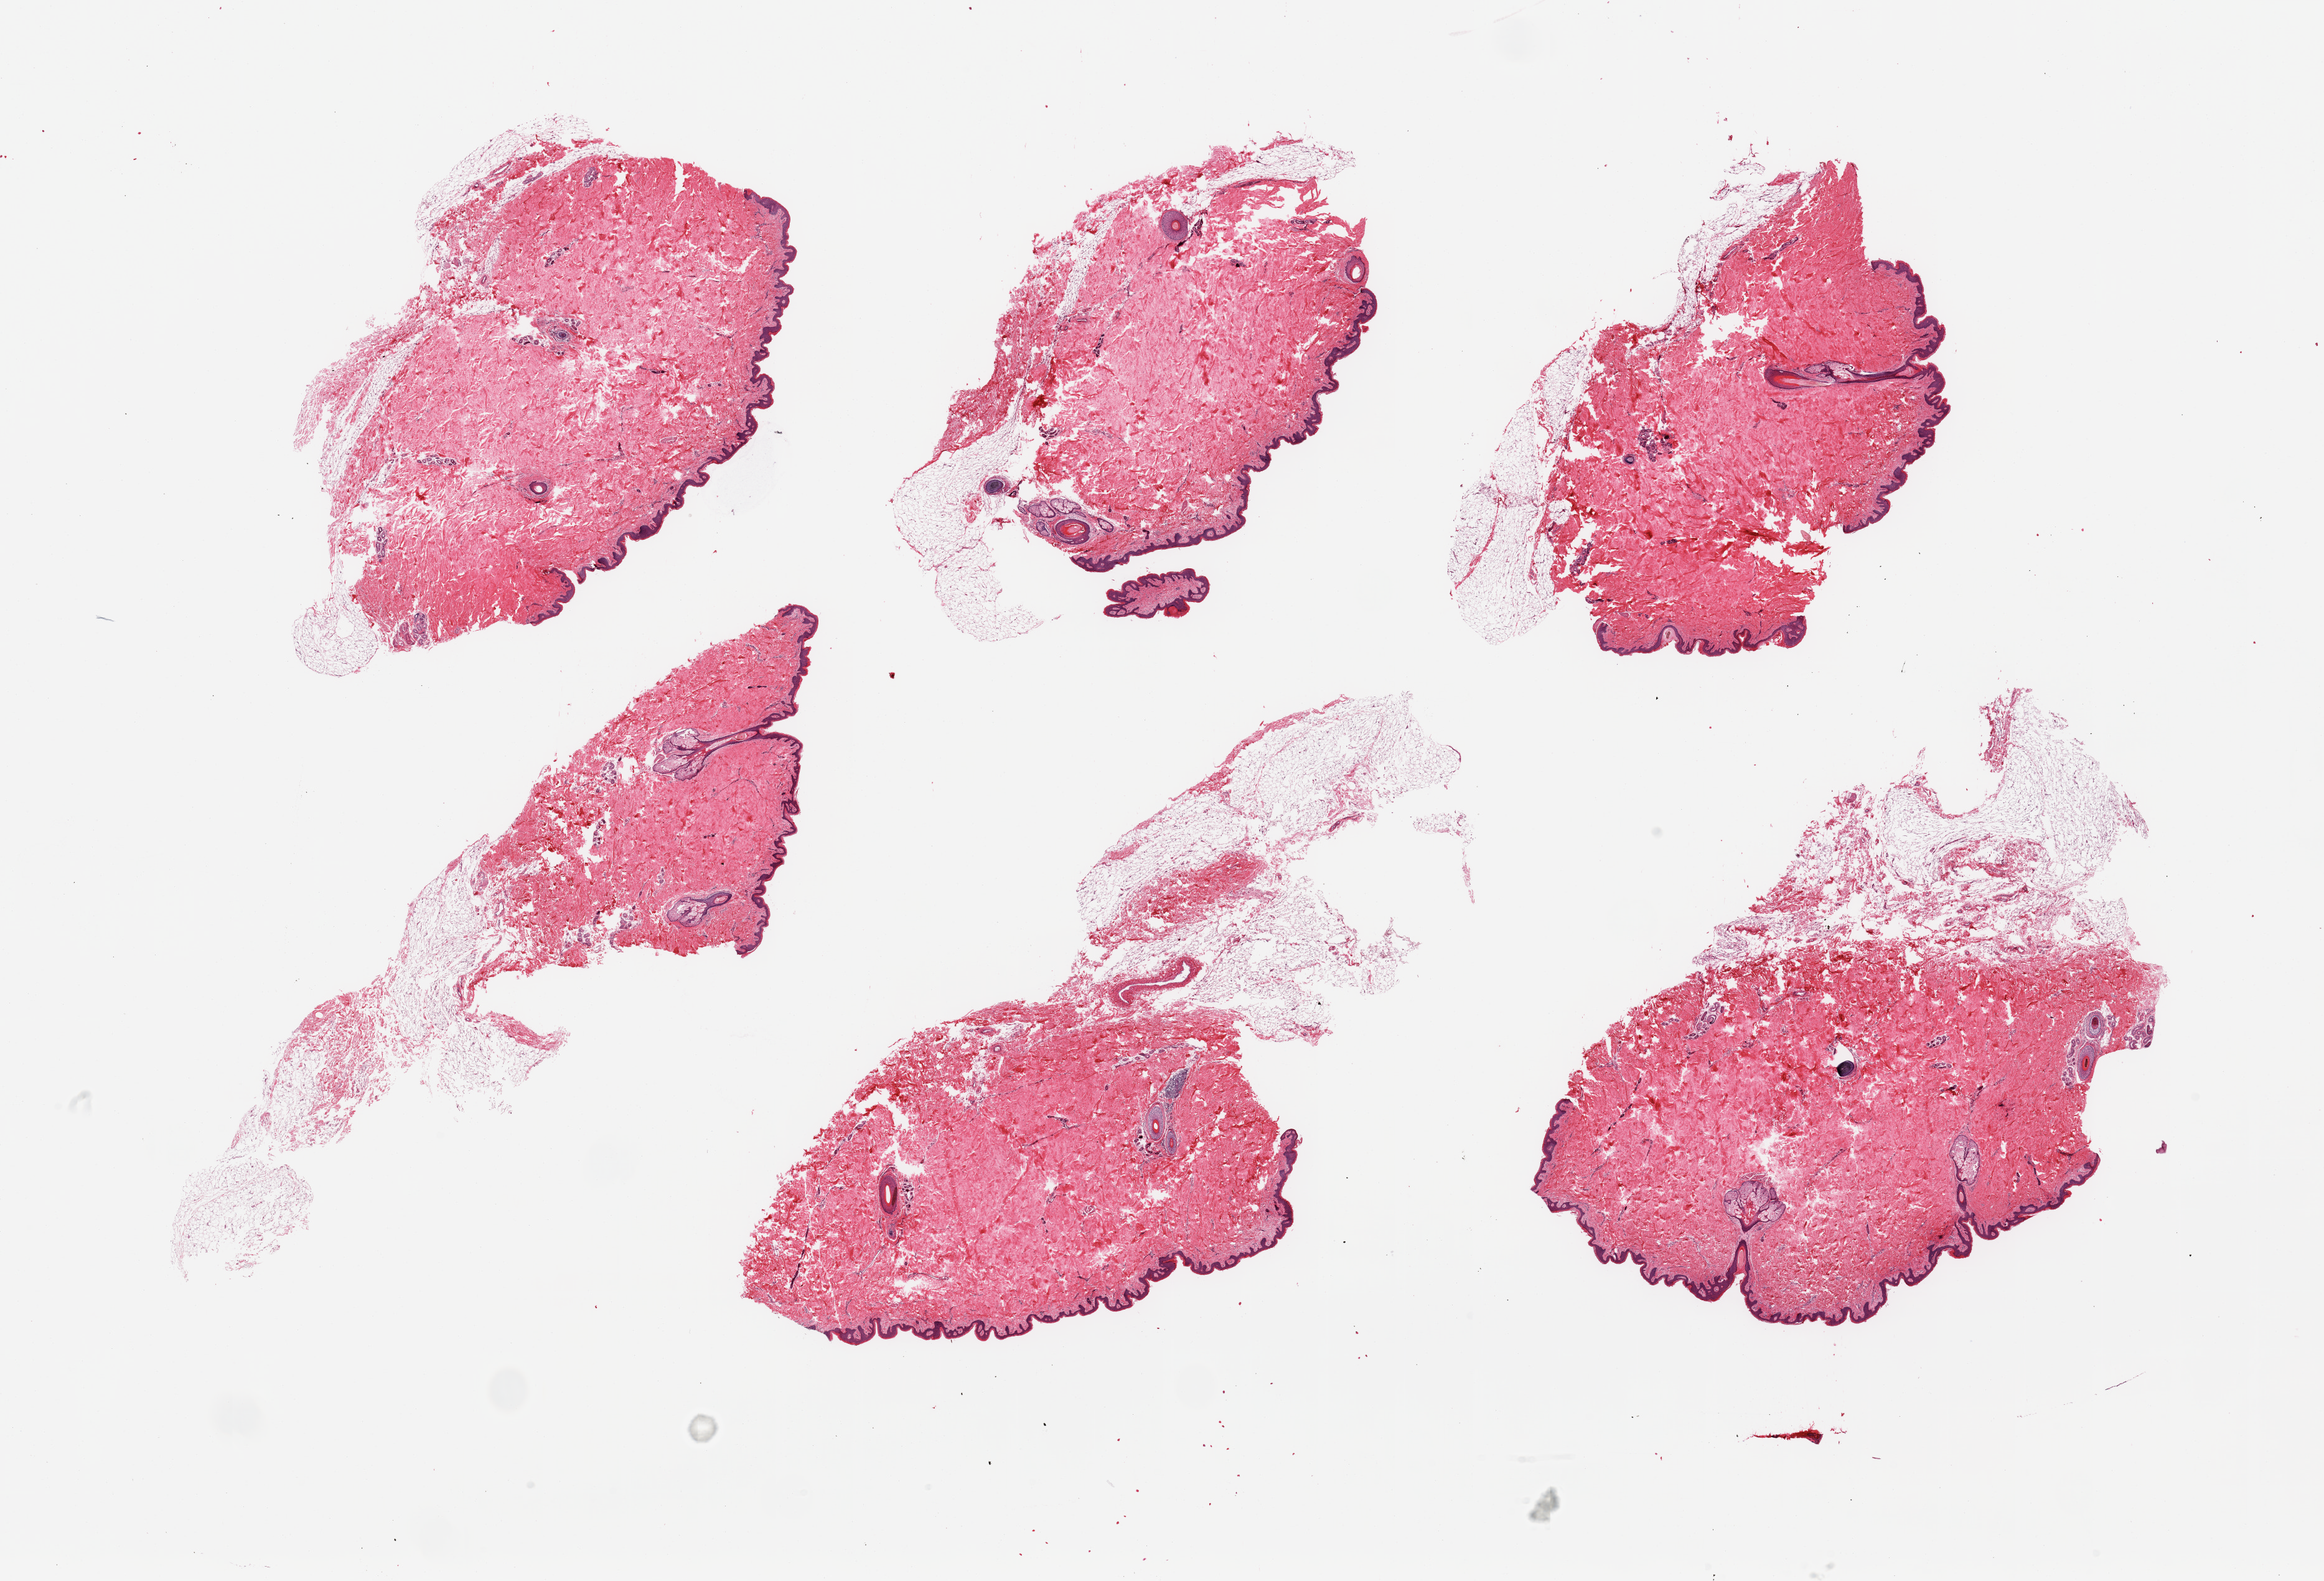
H&E whole-slide image, a low-resolution overview of the entire scanned area, about 29.5 x 20.1 mm (acquisition: 20x scan), PAXgene-fixed, paraffin-embedded tissue, target tissue: skin of suprapubic region, donor tissue sample. Donor sex: male.
Review note (as recorded): 6 pieces, adherent nubbins dermal fat up to ~5mm; squamous epithelium is ~60-70 microns.